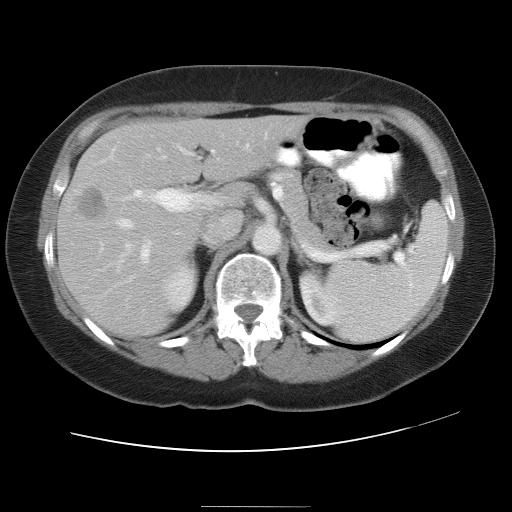
Contrast-enhanced abdominal CT, one axial slice; slice 20 of 30 in the series (ordered by position); reconstruction kernel STANDARD; intravenous contrast given; soft-tissue window (W 400 / L 40 HU); 512 × 512 image matrix, field of view 376 × 376 mm. Female patient, age 52 years. From the clinical record (not read from this slice): diagnosis: colorectal cancer liver metastases, imaged before liver resection; multiple liver metastases: no; largest metastasis: 3 cm; disease in both lobes: yes.
Outlined on this slice (outlined manually by an expert reader):
- hepatic veins: bounding box (x1, y1, x2, y2) in pixels: (116, 149, 164, 228)
- liver: (57, 116, 300, 336)
- planned liver remnant (the part of the liver to remain after resection): (147, 116, 300, 190)
- portal vein (with intrahepatic branches): (101, 143, 250, 266)
- liver metastasis: (131, 157, 137, 163)
- liver metastasis: (80, 189, 109, 221)